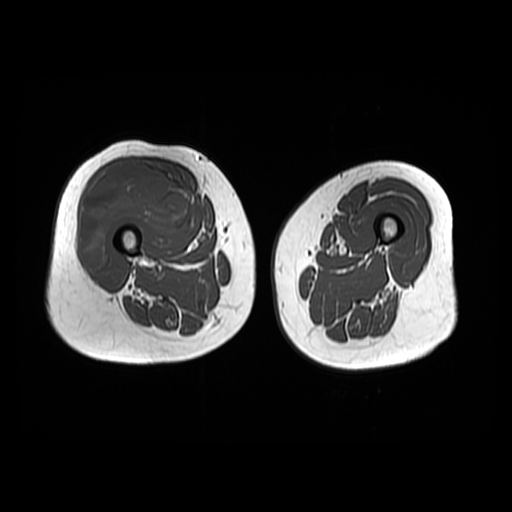
MRI of an extremity soft-tissue mass, one axial slice. Position 23 of 48 along the scan axis. 512 × 512 image matrix. Female patient. From the clinical record (not read from this slice): histological type: pleiomorphic undifferentiated sarcoma; grade: high; site of the primary tumour: right quadricep.
Structures marked on this image (expert manual segmentation):
- gross tumour volume including surrounding oedema: bounding box [x1, y1, x2, y2] px = [81, 161, 191, 267]
- gross tumour volume (mass): [81, 161, 191, 267]